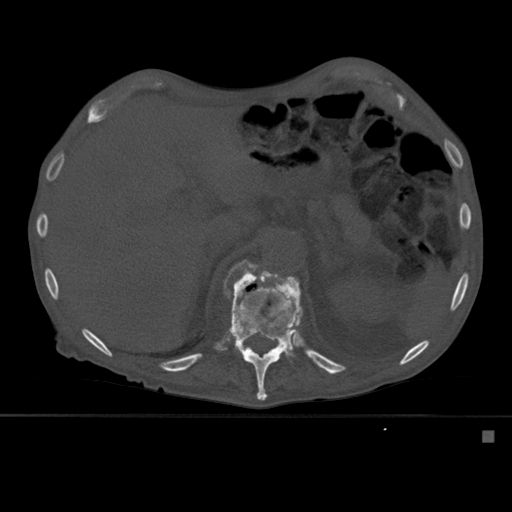
CT including the spine, one axial slice. Slice 274 of 527 in the series (ordered by position). Bone window (W 1800 / L 400 HU). 512 × 512 image matrix. Male patient, age 78 years. Case-level facts recorded for this patient, not image findings: primary cancer: prostate.
Annotated regions visible in this slice (semi-automatic segmentation, software-assisted and operator-edited):
- L1 vertebra: bounding box [x1, y1, x2, y2] px = [252, 265, 258, 269]
- T12 vertebra: [223, 260, 303, 401]